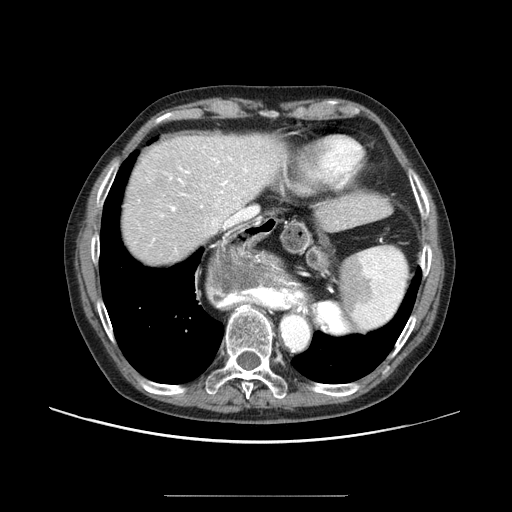
Contrast-enhanced abdominal CT (liver protocol), one axial slice; slice 74 of 91 in the series (ordered by position); reconstruction kernel STANDARD; one of 2 acquisitions stored at this slice position; soft-tissue window (W 400 / L 40 HU); 2.5 mm slice thickness; 512 × 512 image matrix. Case-level facts recorded for this patient, not image findings: diagnosis: hepatocellular carcinoma (patient treated with transarterial chemoembolisation; whether this scan precedes or follows treatment is not stated here); TNM stage (as recorded): Stage-I; Child-Pugh class: A; tumour differentiation: moderately differentiated; tumour nodularity: uninodular.
Annotated regions visible in this slice (semi-automatically segmented with operator editing):
- abdominal aorta: bounding box (x1, y1, x2, y2) in pixels: (281, 315, 308, 348)
- liver parenchyma outside the tumour (the mass and vessels are separate outlines, so this box may not span the whole liver): (122, 134, 284, 264)
- liver vessels: (153, 146, 257, 241)